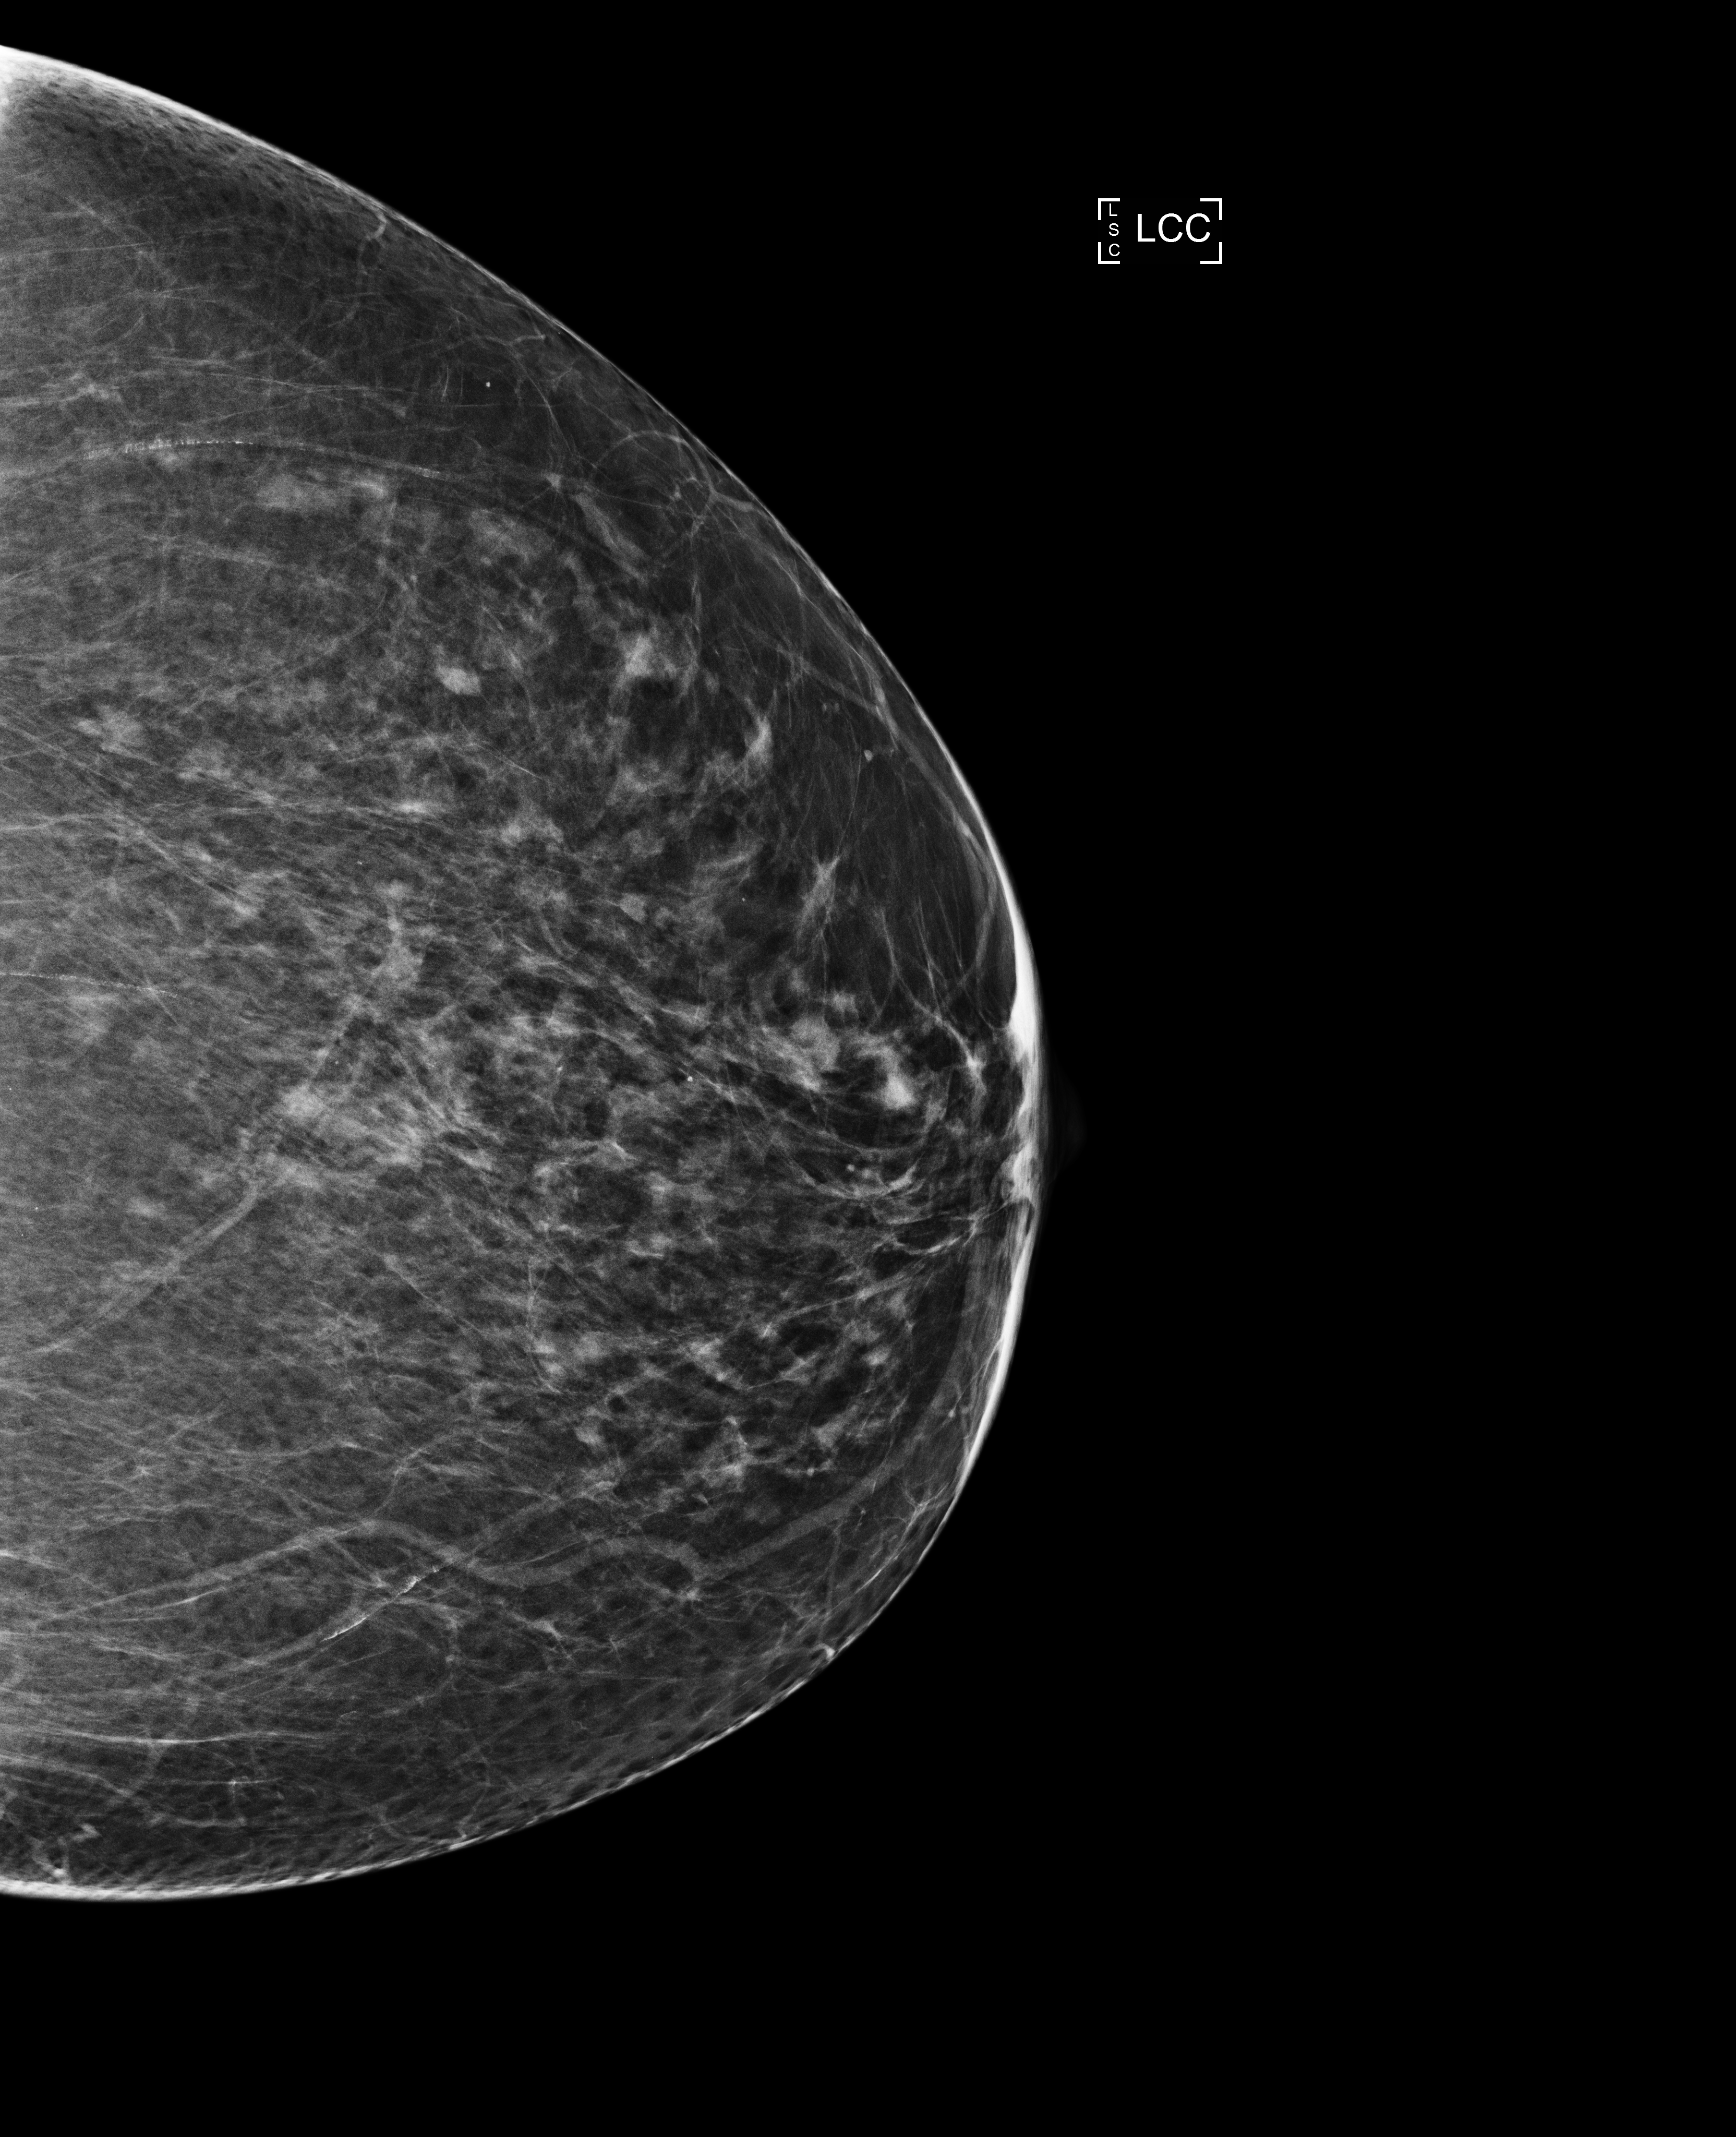
Digital mammogram (FFDM); left breast; cranio-caudal projection; screening examination; compressed breast thickness 64 mm. Patient aged 73 years (female).
BI-RADS breast density category at the screening exam (both breasts, scale 1–4): 3. Final BI-RADS category for the screening round (tomosynthesis exam, both breasts): category 1. Recall: no recall after this screen.